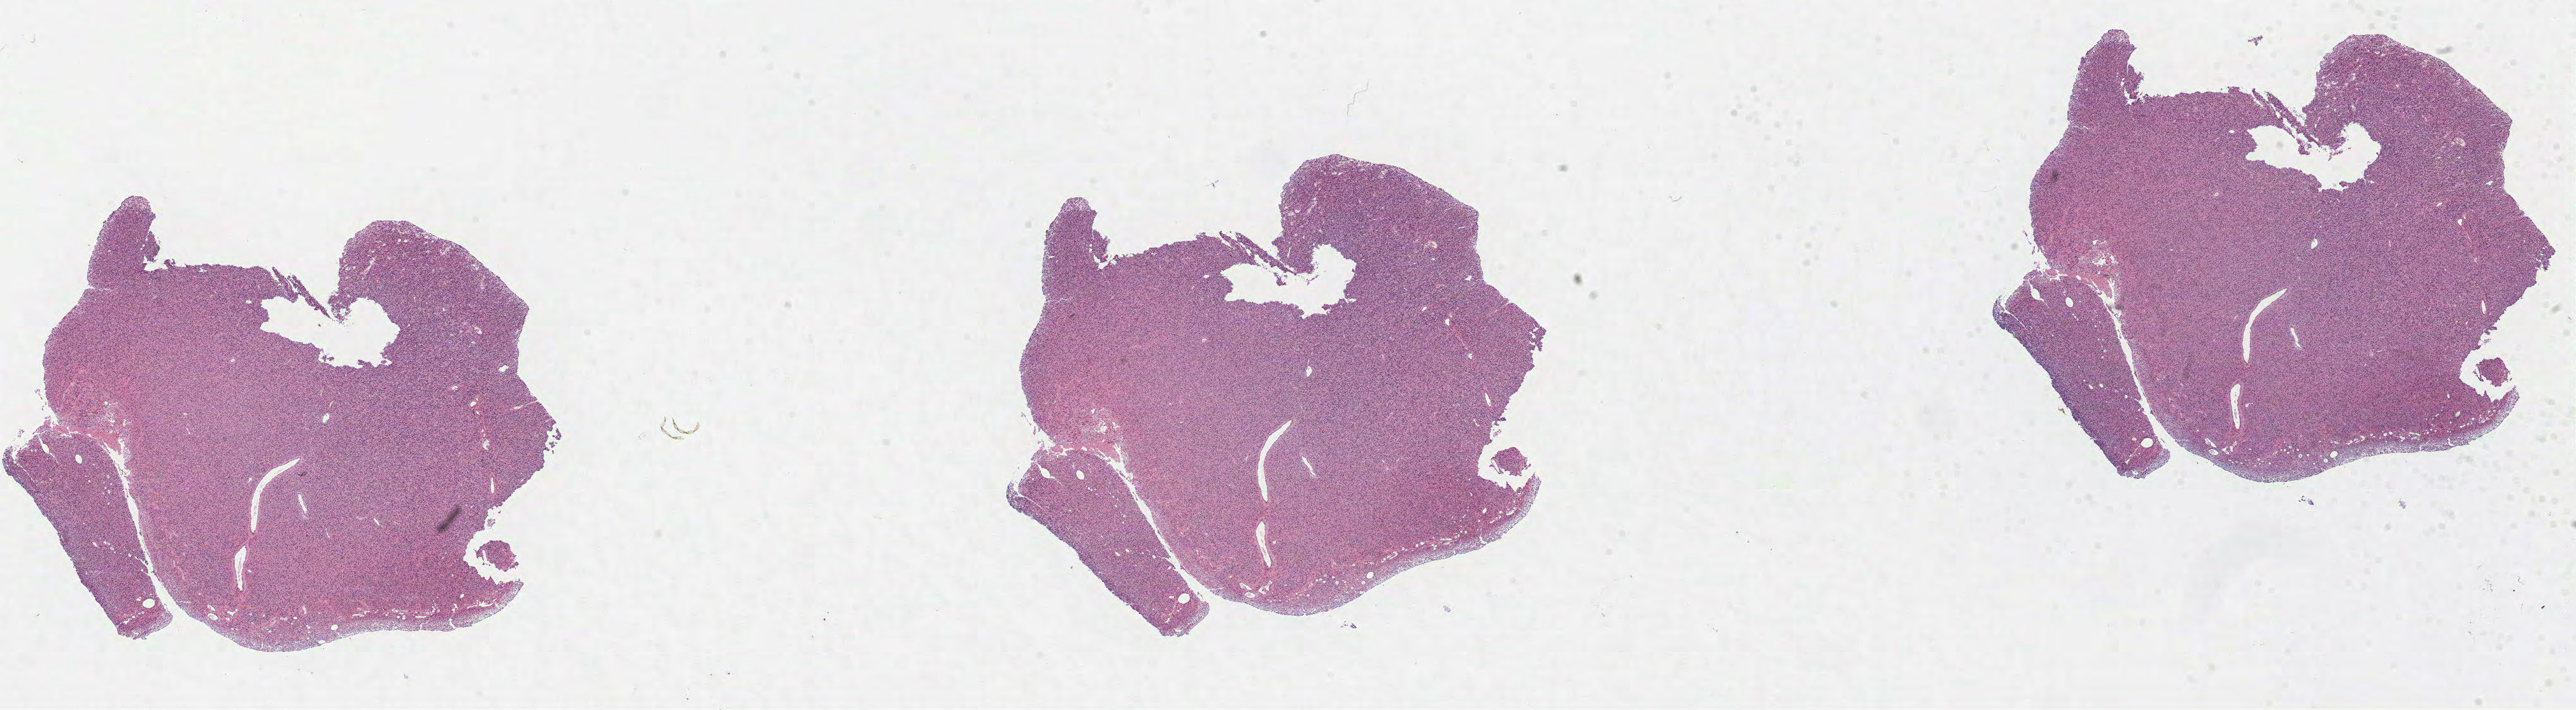
Digitized Hematoxylin and eosin (H&E) stained tissue section (whole slide), a low-resolution overview of the entire scanned area, about 32.6 x 9.0 mm (acquisition: 40x scan); FFPE section; primary tumour sample from the brain. Female, age 59 years at initial diagnosis. Histologic grade: G3 (poorly differentiated).
- pathologic diagnosis: Mixed glioma (cerebrum)